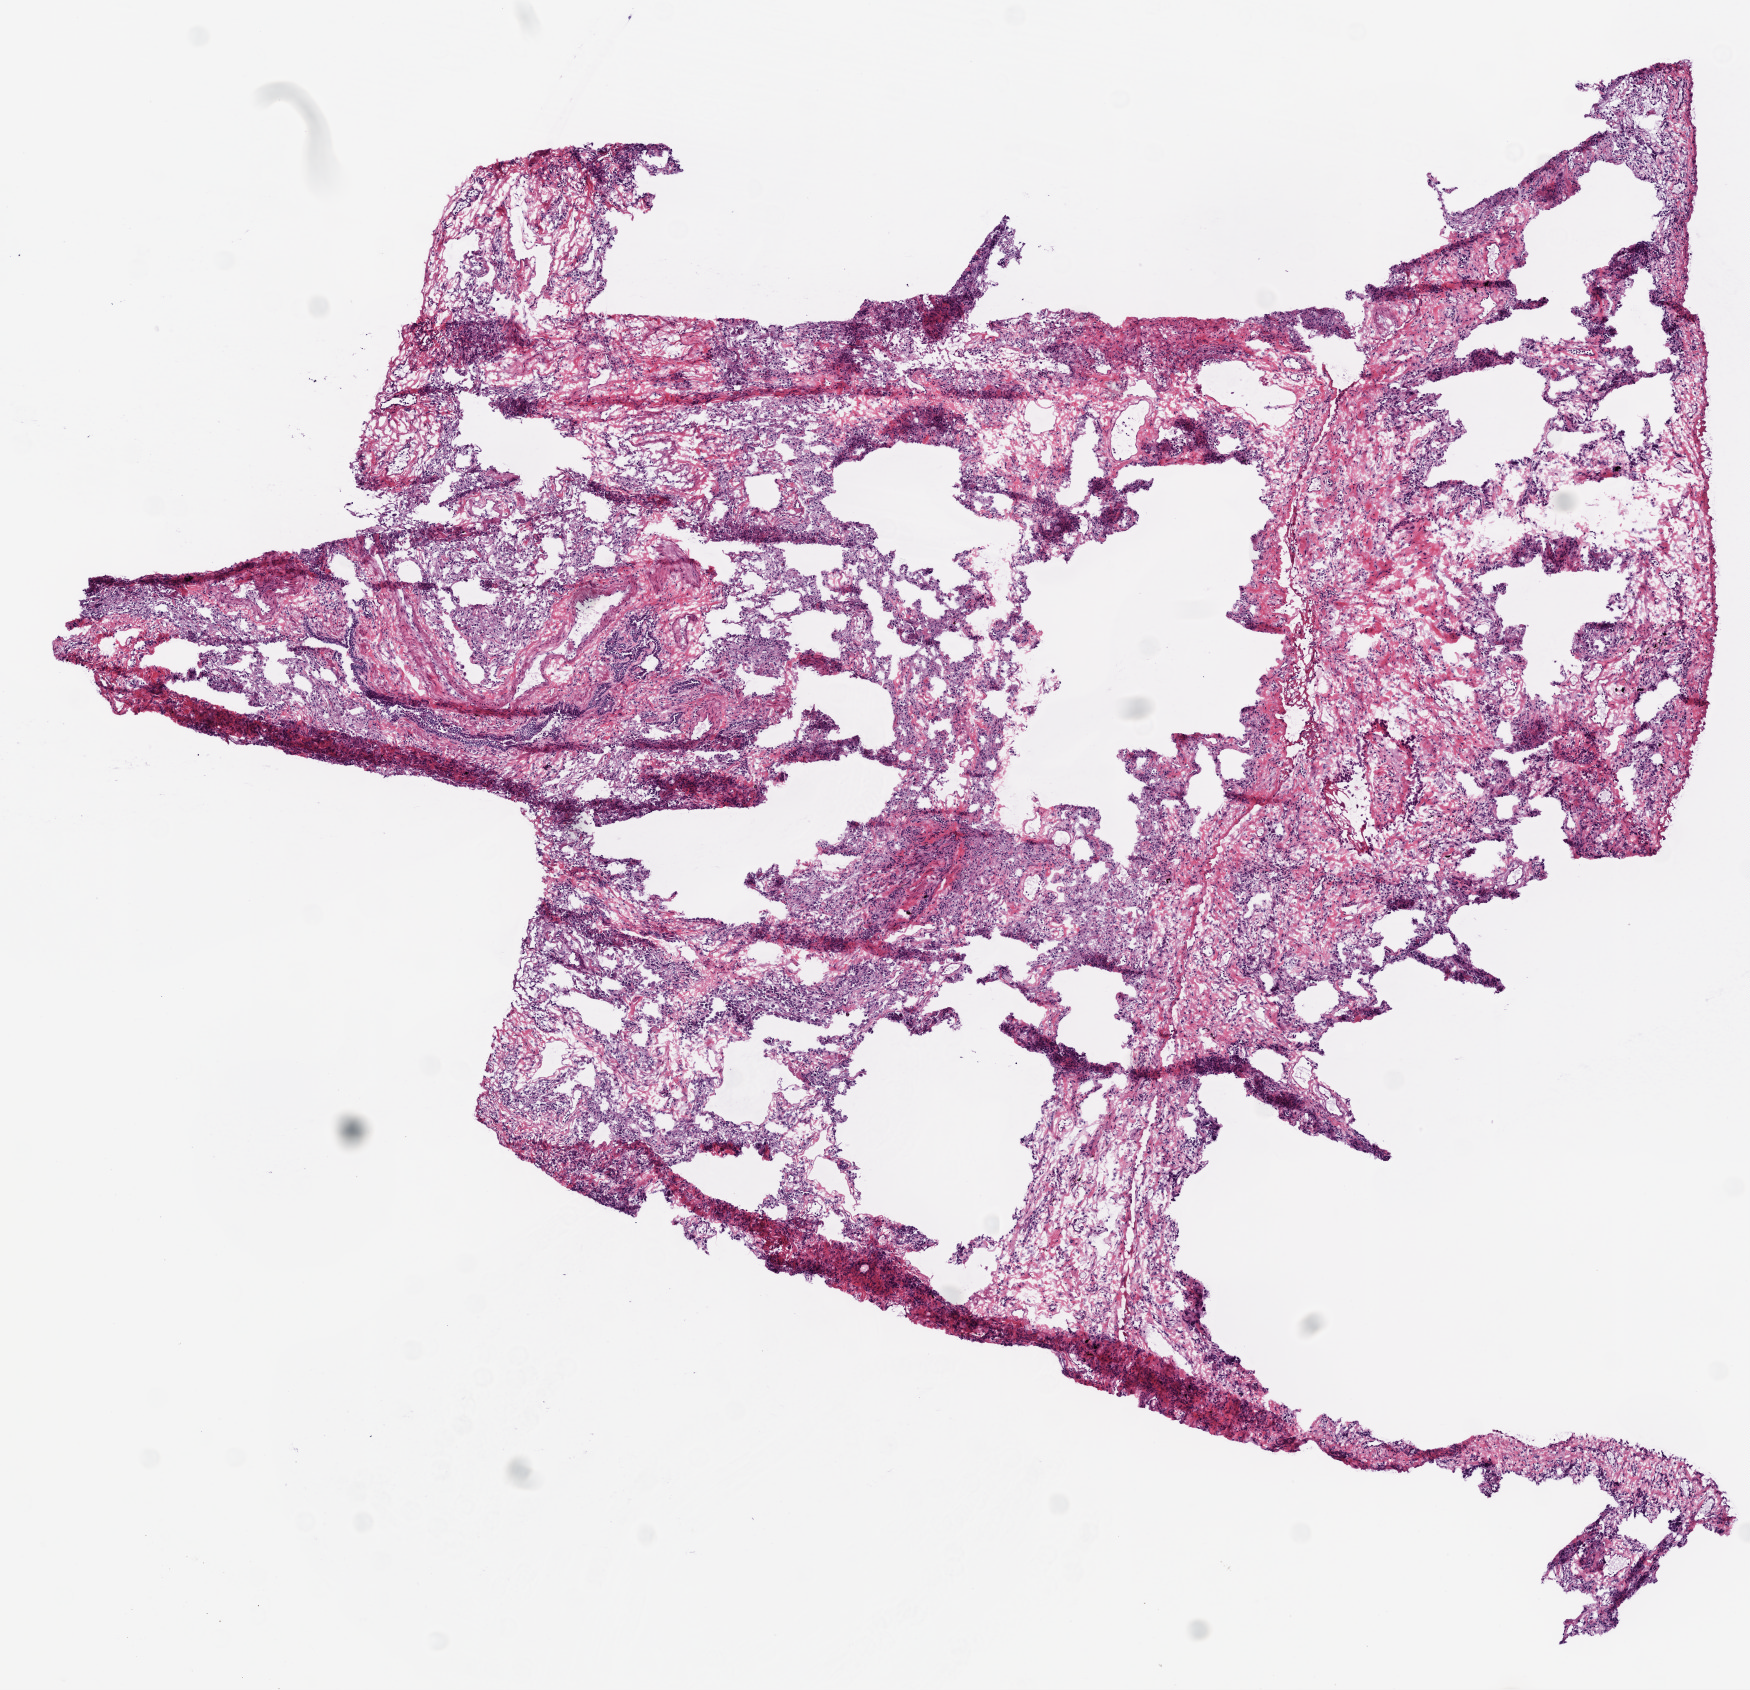
Hematoxylin and eosin (H&E) stained whole-slide image, low-resolution overview of the scanned area, about 7.0 x 6.8 mm, frozen section from the top of the tissue portion, sample: solid tissue normal (non-tumour tissue), lung. Female, age 68 years at initial diagnosis.
• this section: solid tissue normal (non-tumour) sample from the same patient
• patient diagnosis: Squamous cell carcinoma, NOS (lower lobe, lung)